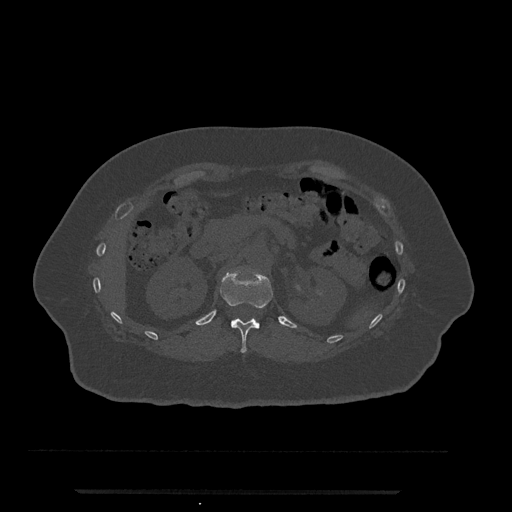
CT including the spine, one axial slice. Position 157 of 797 along the scan axis. Bone window (W 1800 / L 400 HU). 0.5 mm slice thickness. 512 × 512 image matrix, field of view 440 × 440 mm. Patient: female, 51 years. From the clinical record (not read from this slice): primary cancer: neuro; vertebrae with lytic lesions (as recorded): T8.
Structures marked on this image (semi-automatically segmented with operator editing):
- T12 vertebra: bounding box <220,268,273,353> (left, top, right, bottom; pixels)